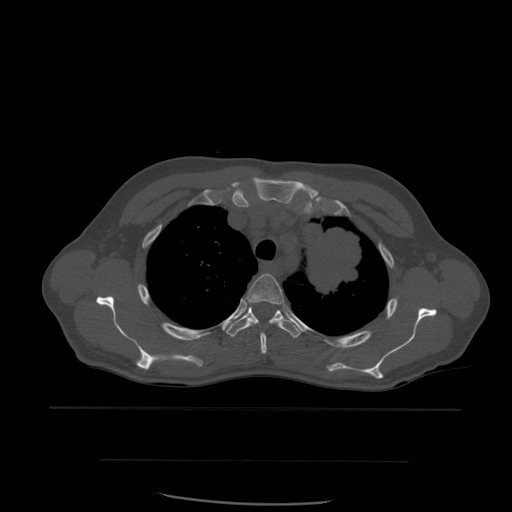
CT including the spine, one axial slice. Slice 434 of 574 in the series (ordered by position). Bone window (W 1800 / L 400 HU). 1.25 mm slice thickness. 512 × 512 image matrix, field of view 392 × 392 mm. Patient age 48 years. From the clinical record (not read from this slice): primary cancer: lung; vertebrae with lytic lesions (as recorded): T11.
Structures marked on this image (semi-automatically segmented with operator editing):
- T3 vertebra: bounding box (x1, y1, x2, y2) in pixels: (244, 274, 285, 354)
- T4 vertebra: (226, 306, 302, 338)
- T5 vertebra: (275, 297, 285, 305)